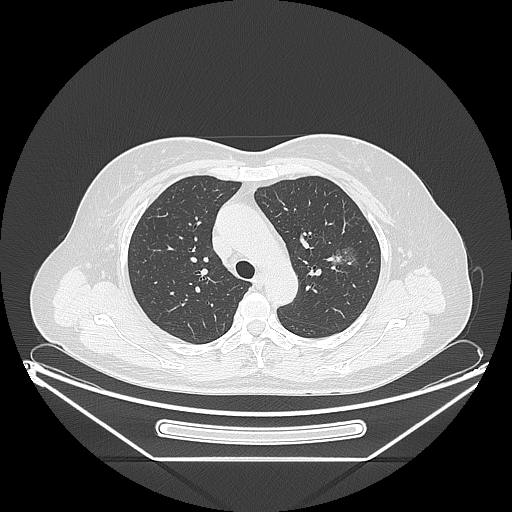
Chest CT, one axial slice; 120 kVp; lung window (W 1500 / L -600 HU); 512 × 512 image matrix, field of view 447 × 447 mm. Patient: female, 54 years. From the clinical record (not read from this slice): clinical TNM (as recorded): T1c N0 M0.
Outlined on this slice (rectangle marked by the reading radiologist):
- lung tumour (recorded histology: adenocarcinoma): box from (x=324, y=237) to (x=357, y=280) px